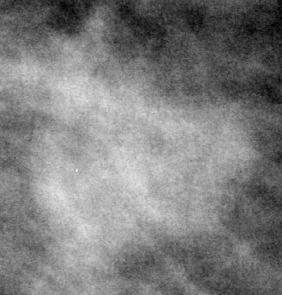
Crop from a digitized film mammogram around one marked abnormality; left breast; MLO view; BI-RADS breast density category 3 (scale 1–4).
Finding: mass, shape lobulated, margins circumscribed / ill defined; BI-RADS assessment category 3; pathology result (as recorded, not read from the image): malignant.